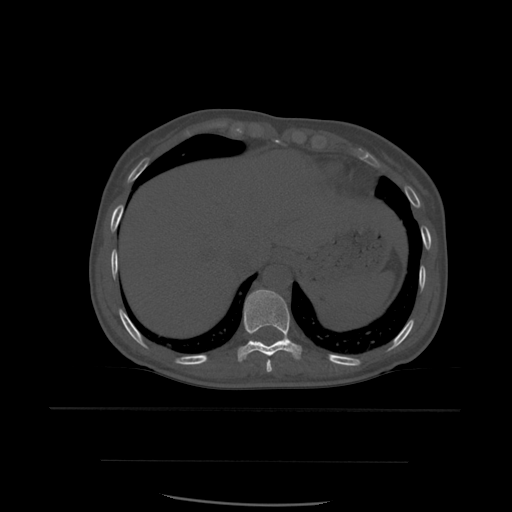
CT including the spine, one axial slice; slice 316 of 574 in the series (ordered by position); bone window (W 1800 / L 400 HU); 512 × 512 image matrix, field of view 392 × 392 mm. Patient age 48 years. From the clinical record (not read from this slice): primary cancer: lung; vertebrae with lytic lesions (as recorded): T11.
Annotated regions visible in this slice (semi-automatic segmentation, software-assisted and operator-edited):
- T10 vertebra: bounding box [x1, y1, x2, y2] px = [238, 290, 302, 363]
- T11 vertebra: [262, 343, 265, 346]
- T9 vertebra: [267, 359, 273, 373]